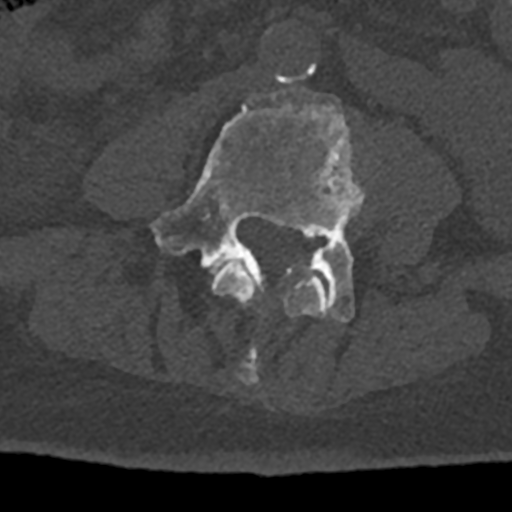
CT including the spine, one axial slice; position 275 of 797 along the scan axis; reconstruction kernel Br40s/3; bone window (W 1800 / L 400 HU); 512 × 512 image matrix, field of view 160 × 160 mm. Patient: male, 74 years. Case-level facts recorded for this patient, not image findings: primary cancer: renal.
Annotated regions visible in this slice (semi-automatically segmented with operator editing):
- L3 vertebra: box from (x=211, y=260) to (x=329, y=385) px
- L4 vertebra: (x=149, y=88)–(x=364, y=323)